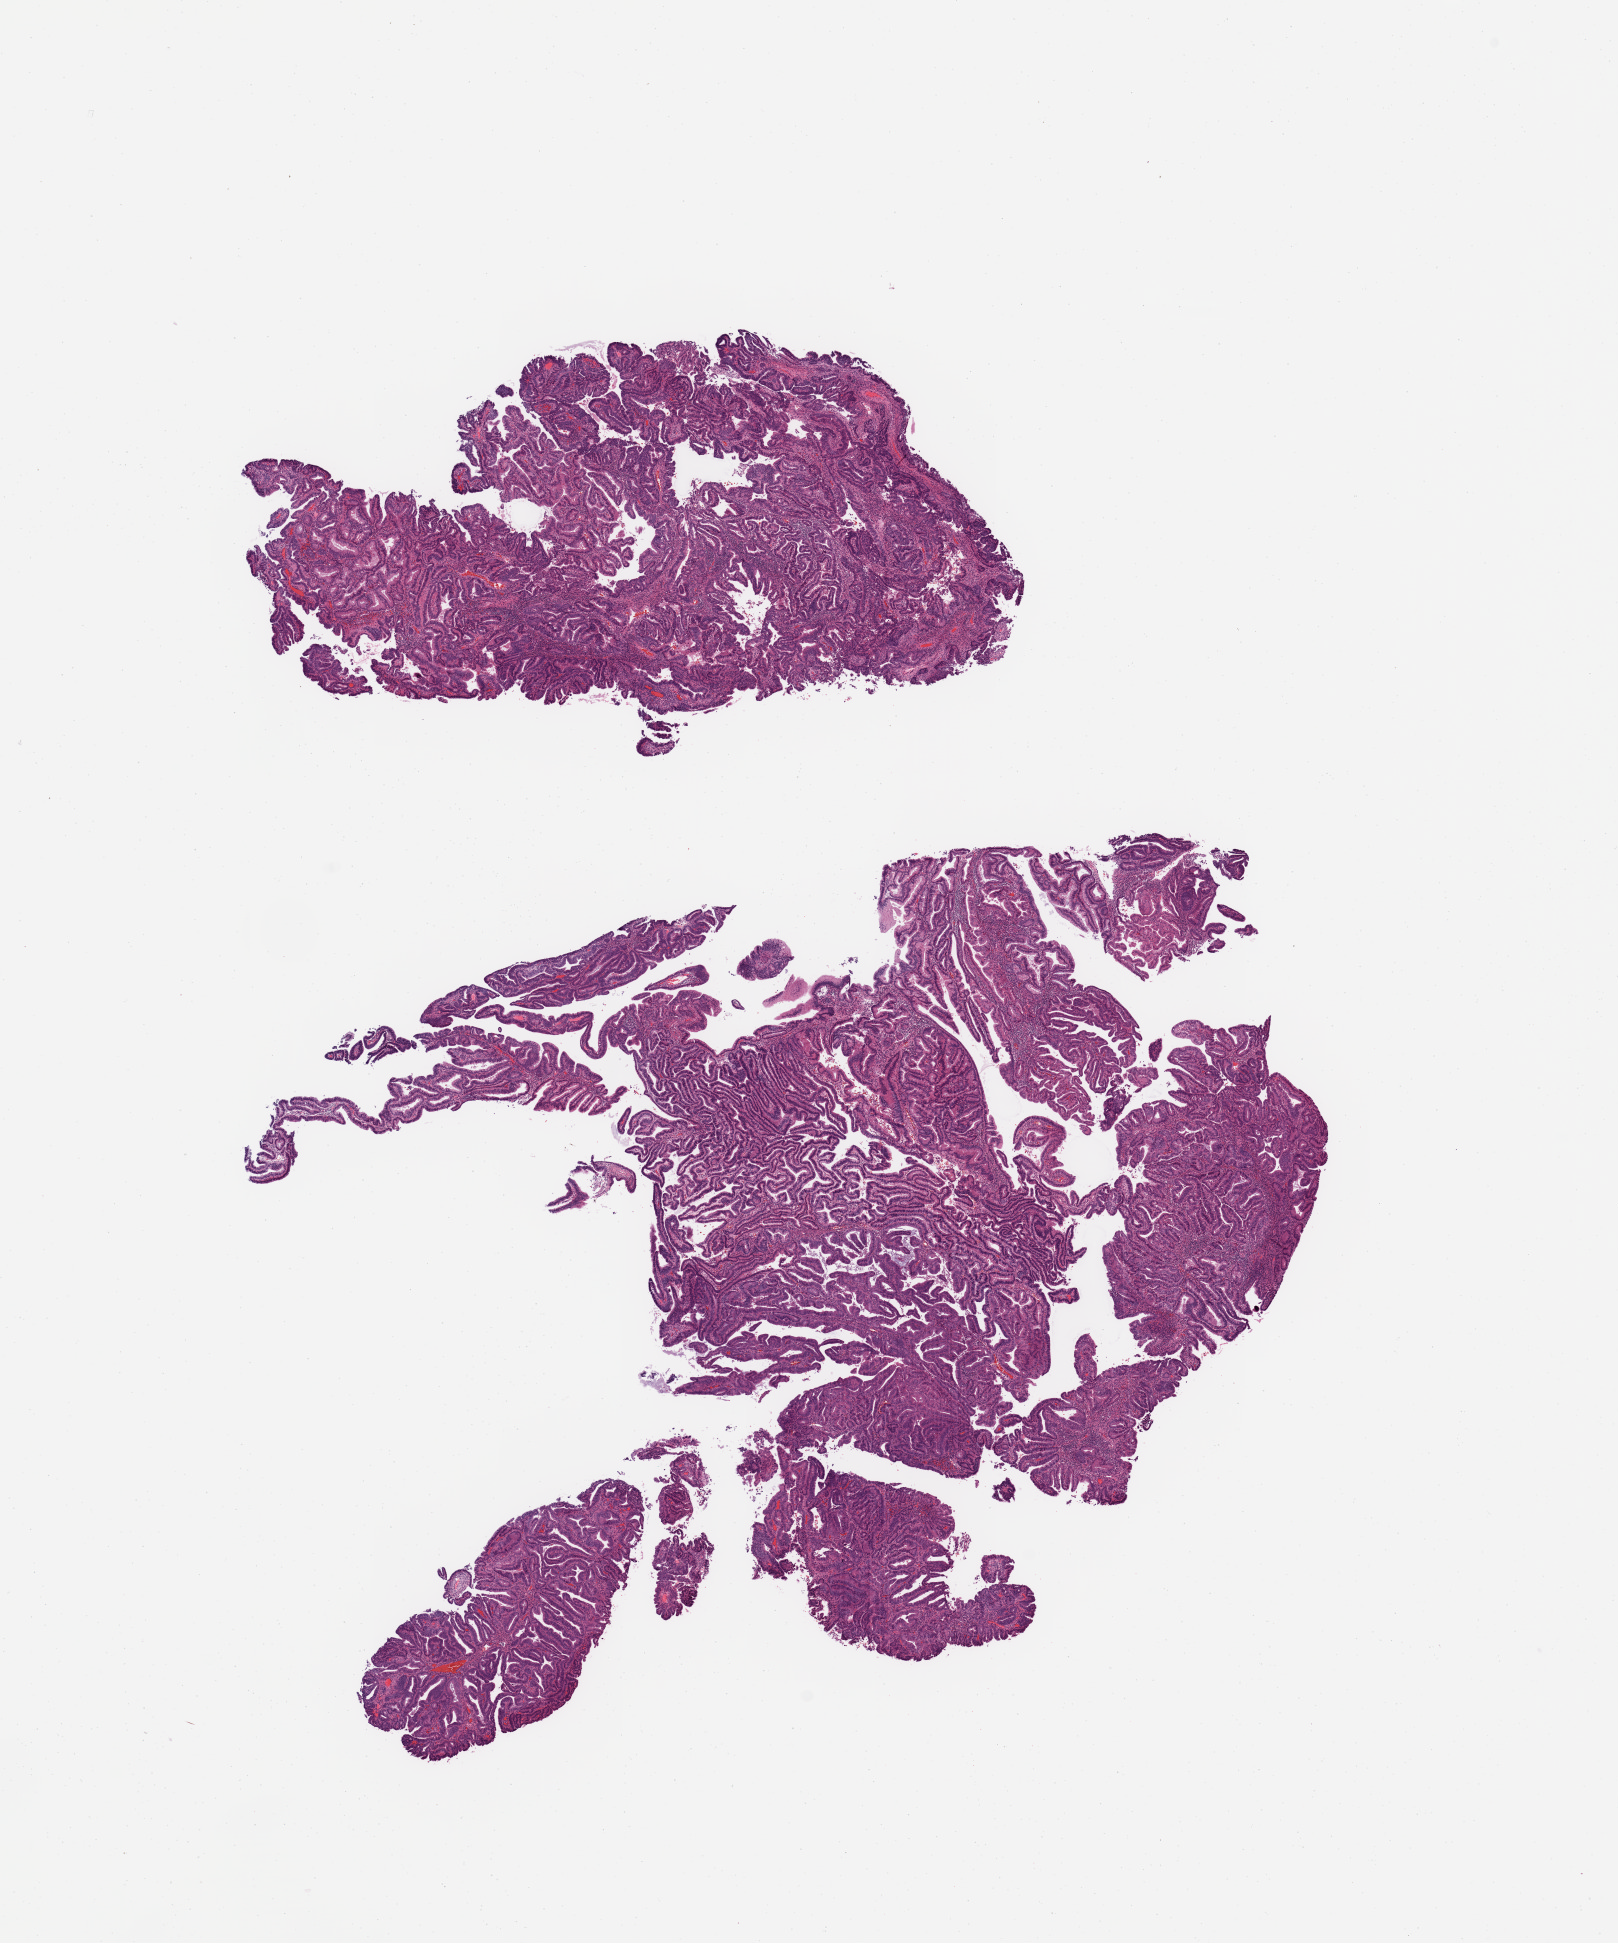
Whole-slide histology image, H&E — low-resolution overview of the scanned area, about 12.8 x 15.4 mm (slide scanned at 20x). Uterus, tumour tissue. 50-year-old female patient. Histologic grade: G1 (well differentiated).
- histologic diagnosis: Endometrioid adenocarcinoma, NOS
- AJCC pathologic stage: III